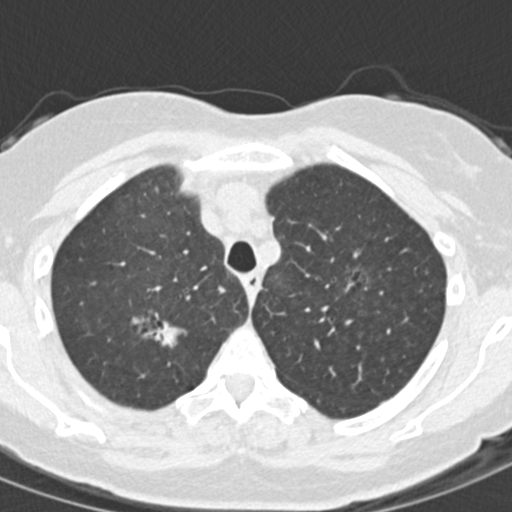
Low-dose screening chest CT, one axial slice. Position 120 of 157 along the scan axis. 120 kVp. Lung window (W 1500 / L -600 HU). 2 mm slice thickness. 512 × 512 image matrix, field of view 280 × 280 mm.
Outlined on this slice (expert manual segmentation):
- lesion 1 (tumor, upper lobe of right lung): box from (x=131, y=308) to (x=188, y=349) px